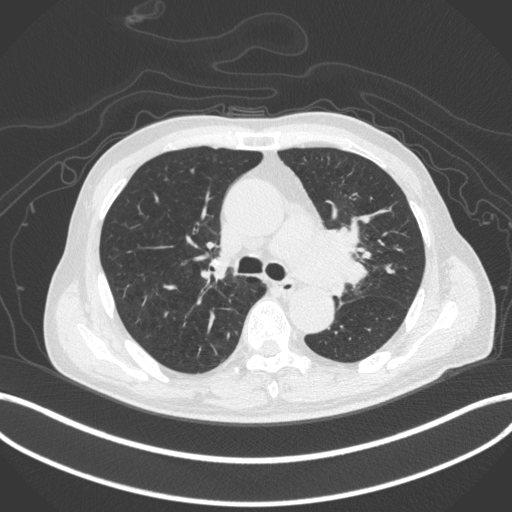
Chest CT, one axial slice; position 281 of 420 along the scan axis; reconstruction kernel B31f; 120 kVp; lung window (W 1500 / L -600 HU); 1 mm slice thickness; 512 × 512 image matrix, field of view 400 × 400 mm. Male patient, age 77 years. Case-level facts recorded for this patient, not image findings: clinical TNM (as recorded): T3 N1 M0.
Outlined on this slice (rectangle marked by the reading radiologist):
- lung tumour (recorded histology: adenocarcinoma): box from (x=301, y=223) to (x=372, y=296) px